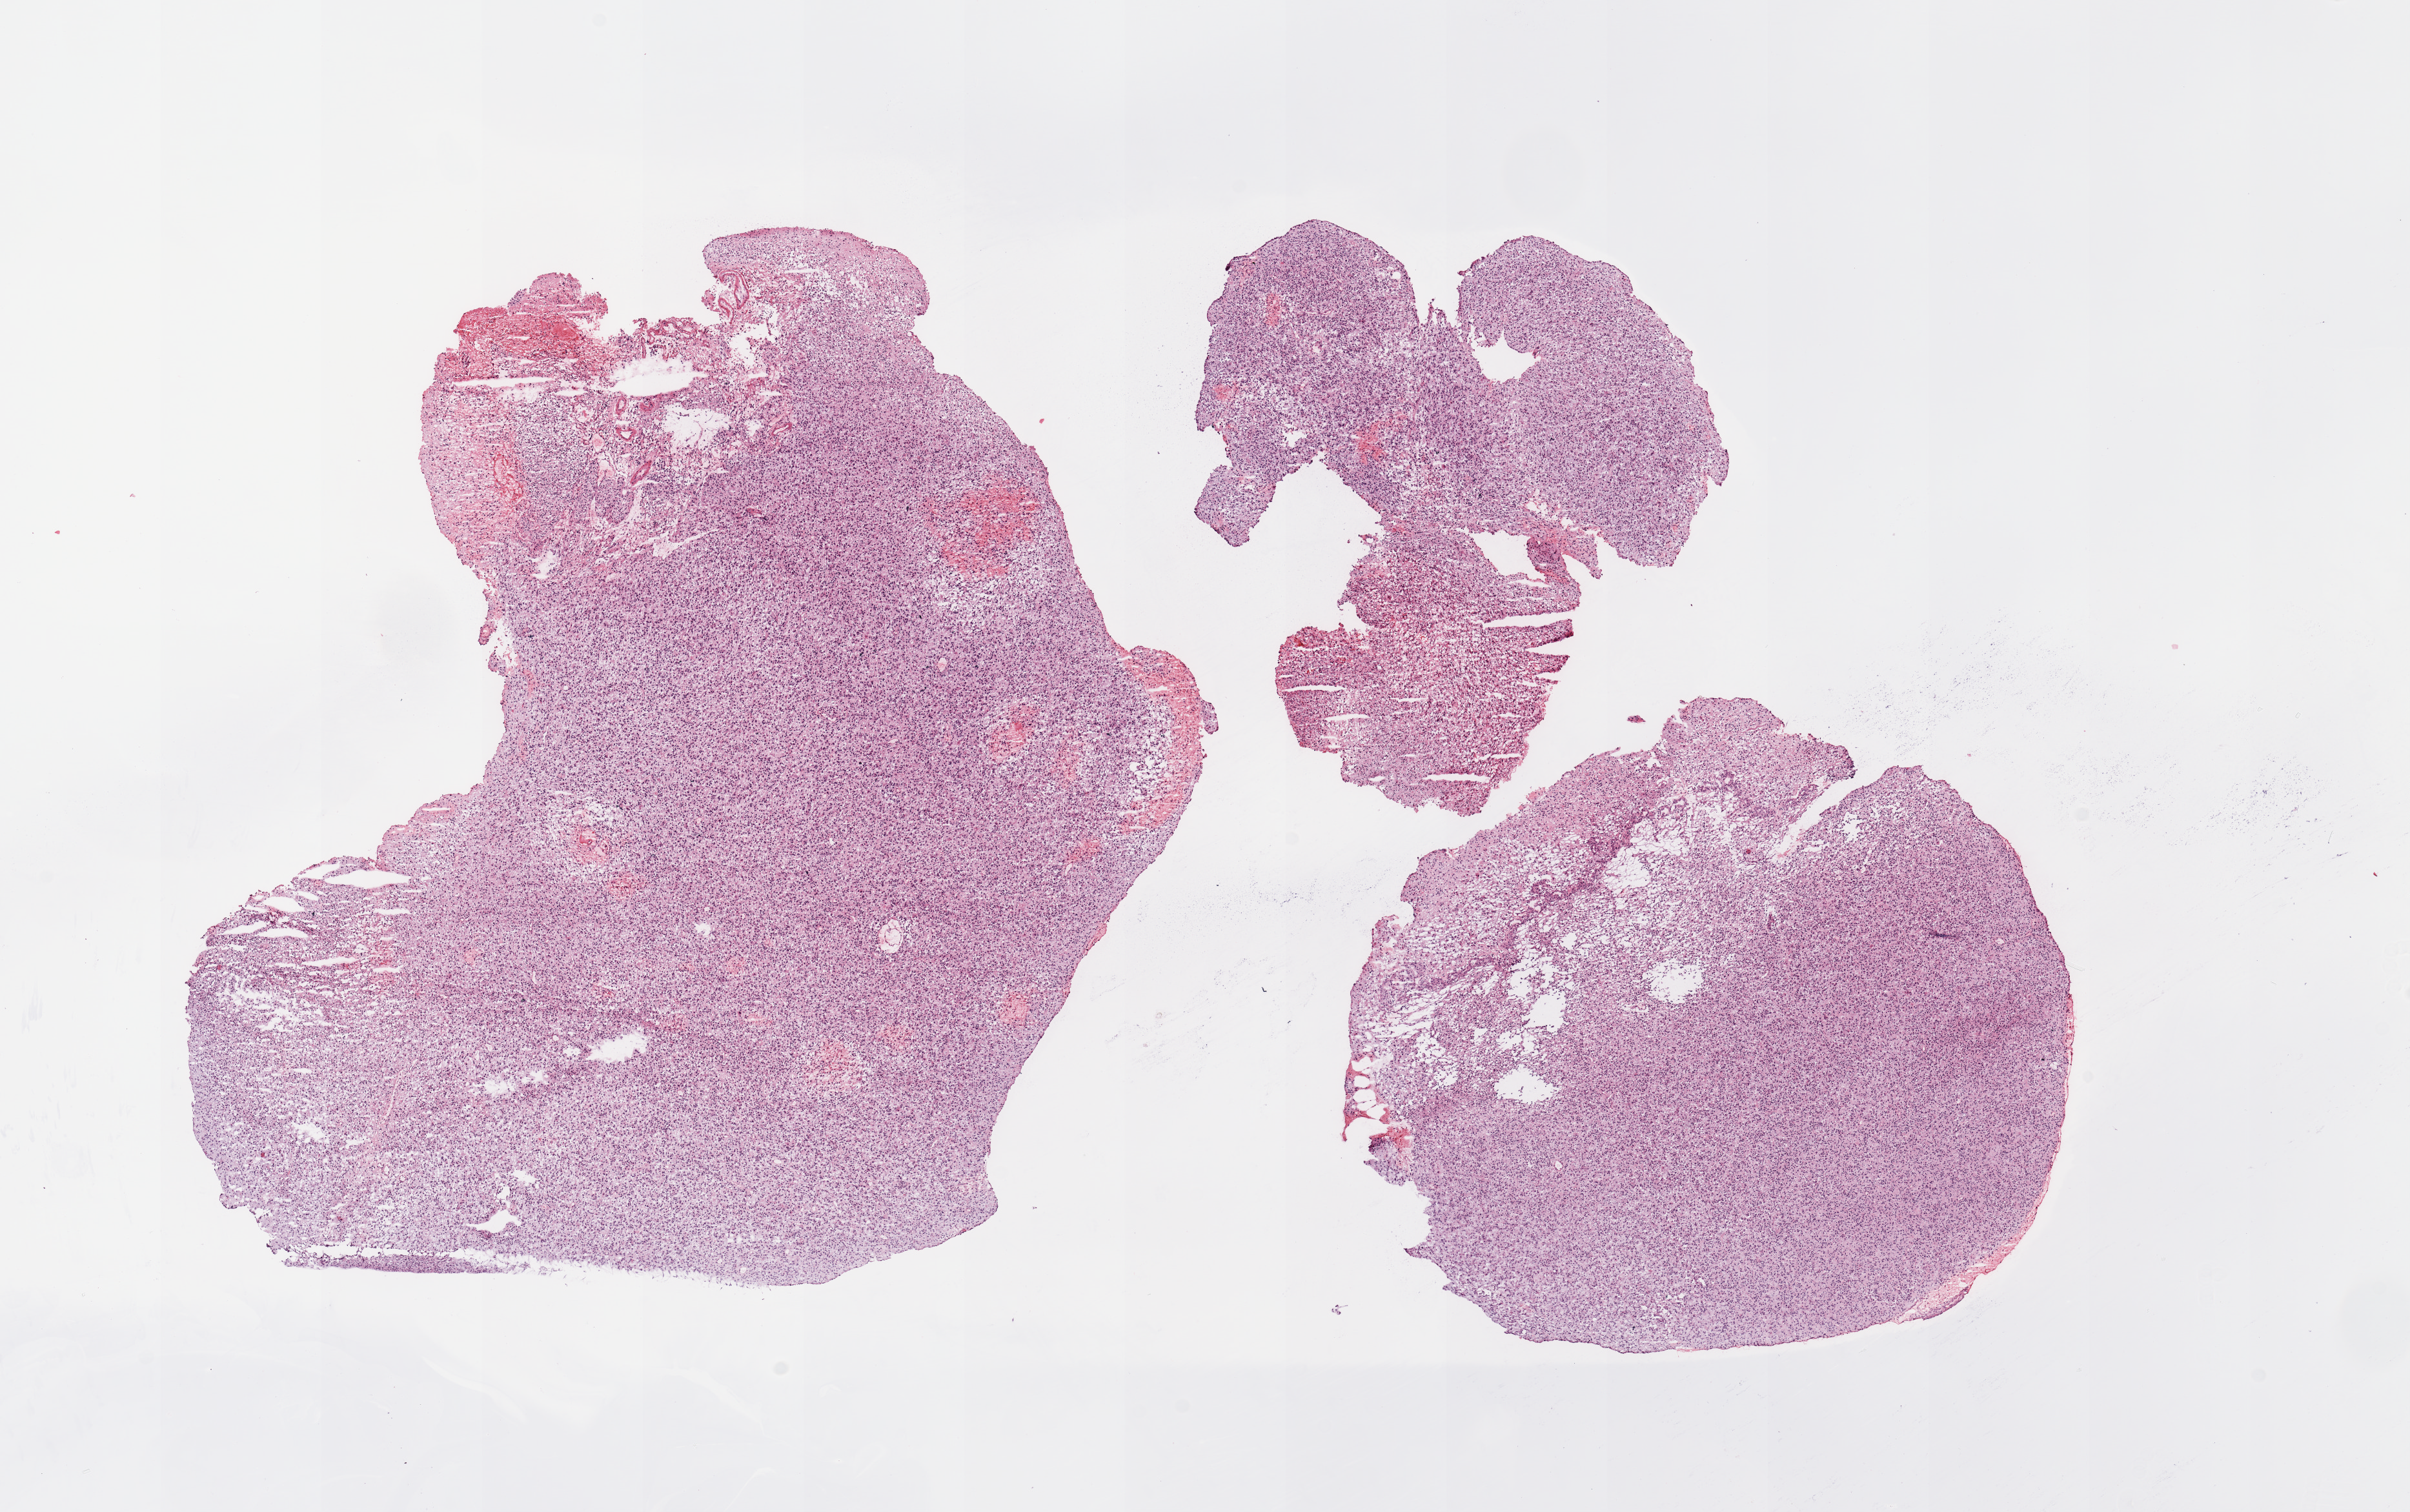
Whole-slide histology image, Hematoxylin and eosin (H&E) stained — a low-resolution overview of the entire scanned area, about 14.8 x 9.3 mm (from a 20x scan); tumour tissue sample, brain. 60-year-old male patient.
Patient diagnosis (cohort enrolment): glioblastoma multiforme (brain).